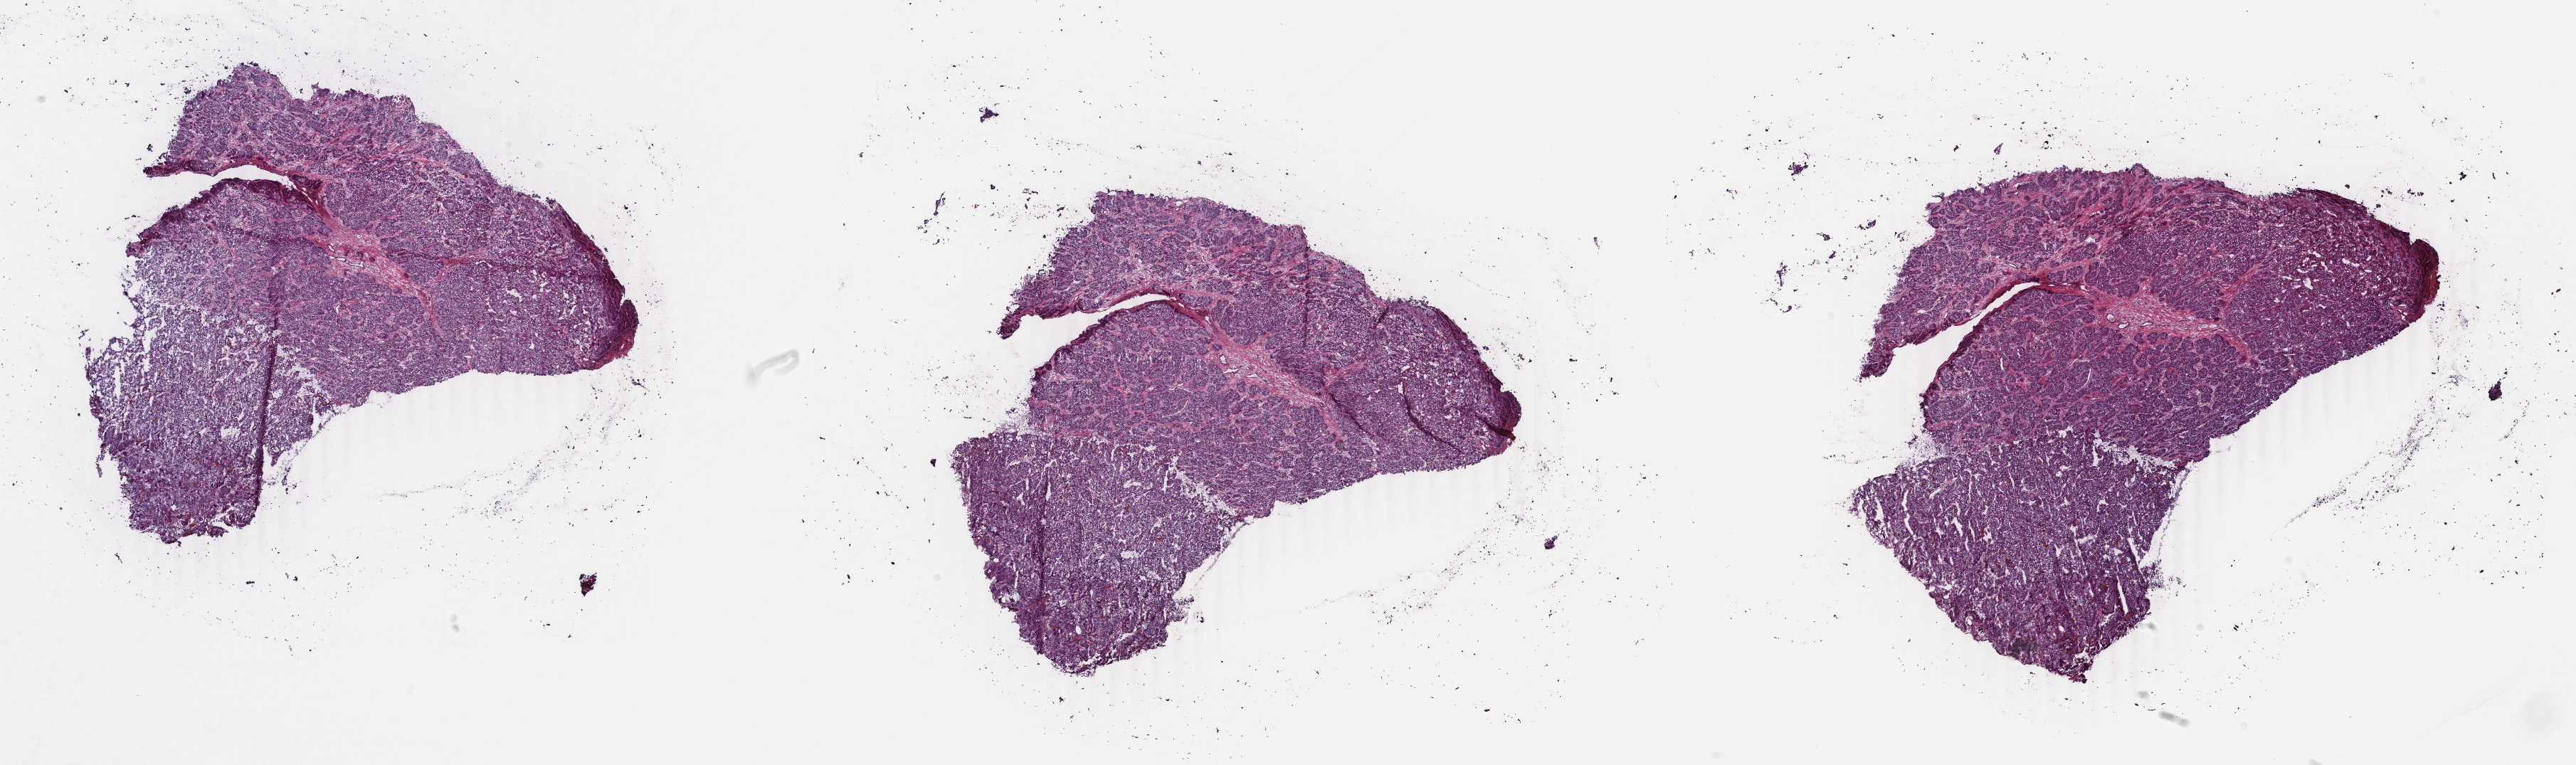
Hematoxylin and eosin (H&E) stained whole-slide image, low-resolution overview of the scanned area, about 28.8 x 8.6 mm (slide scanned at 40x); frozen section from the bottom of the tissue portion; liver, primary tumour sample. Male patient; age at initial diagnosis 40 years. Histologic grade: G3 (poorly differentiated). Composition of this section per pathologist review: tumour cells 90%, tumour nuclei 90%, normal cells 0%, stromal cells 10%, necrosis 0%. Infiltration values recorded for this section: lymphocyte infiltration 1%, monocyte infiltration 1%, neutrophil infiltration 0%.
TNM: T3a N0 M1. AJCC pathologic stage: IV (6th edition). Pathologic diagnosis: Hepatocellular carcinoma, NOS.